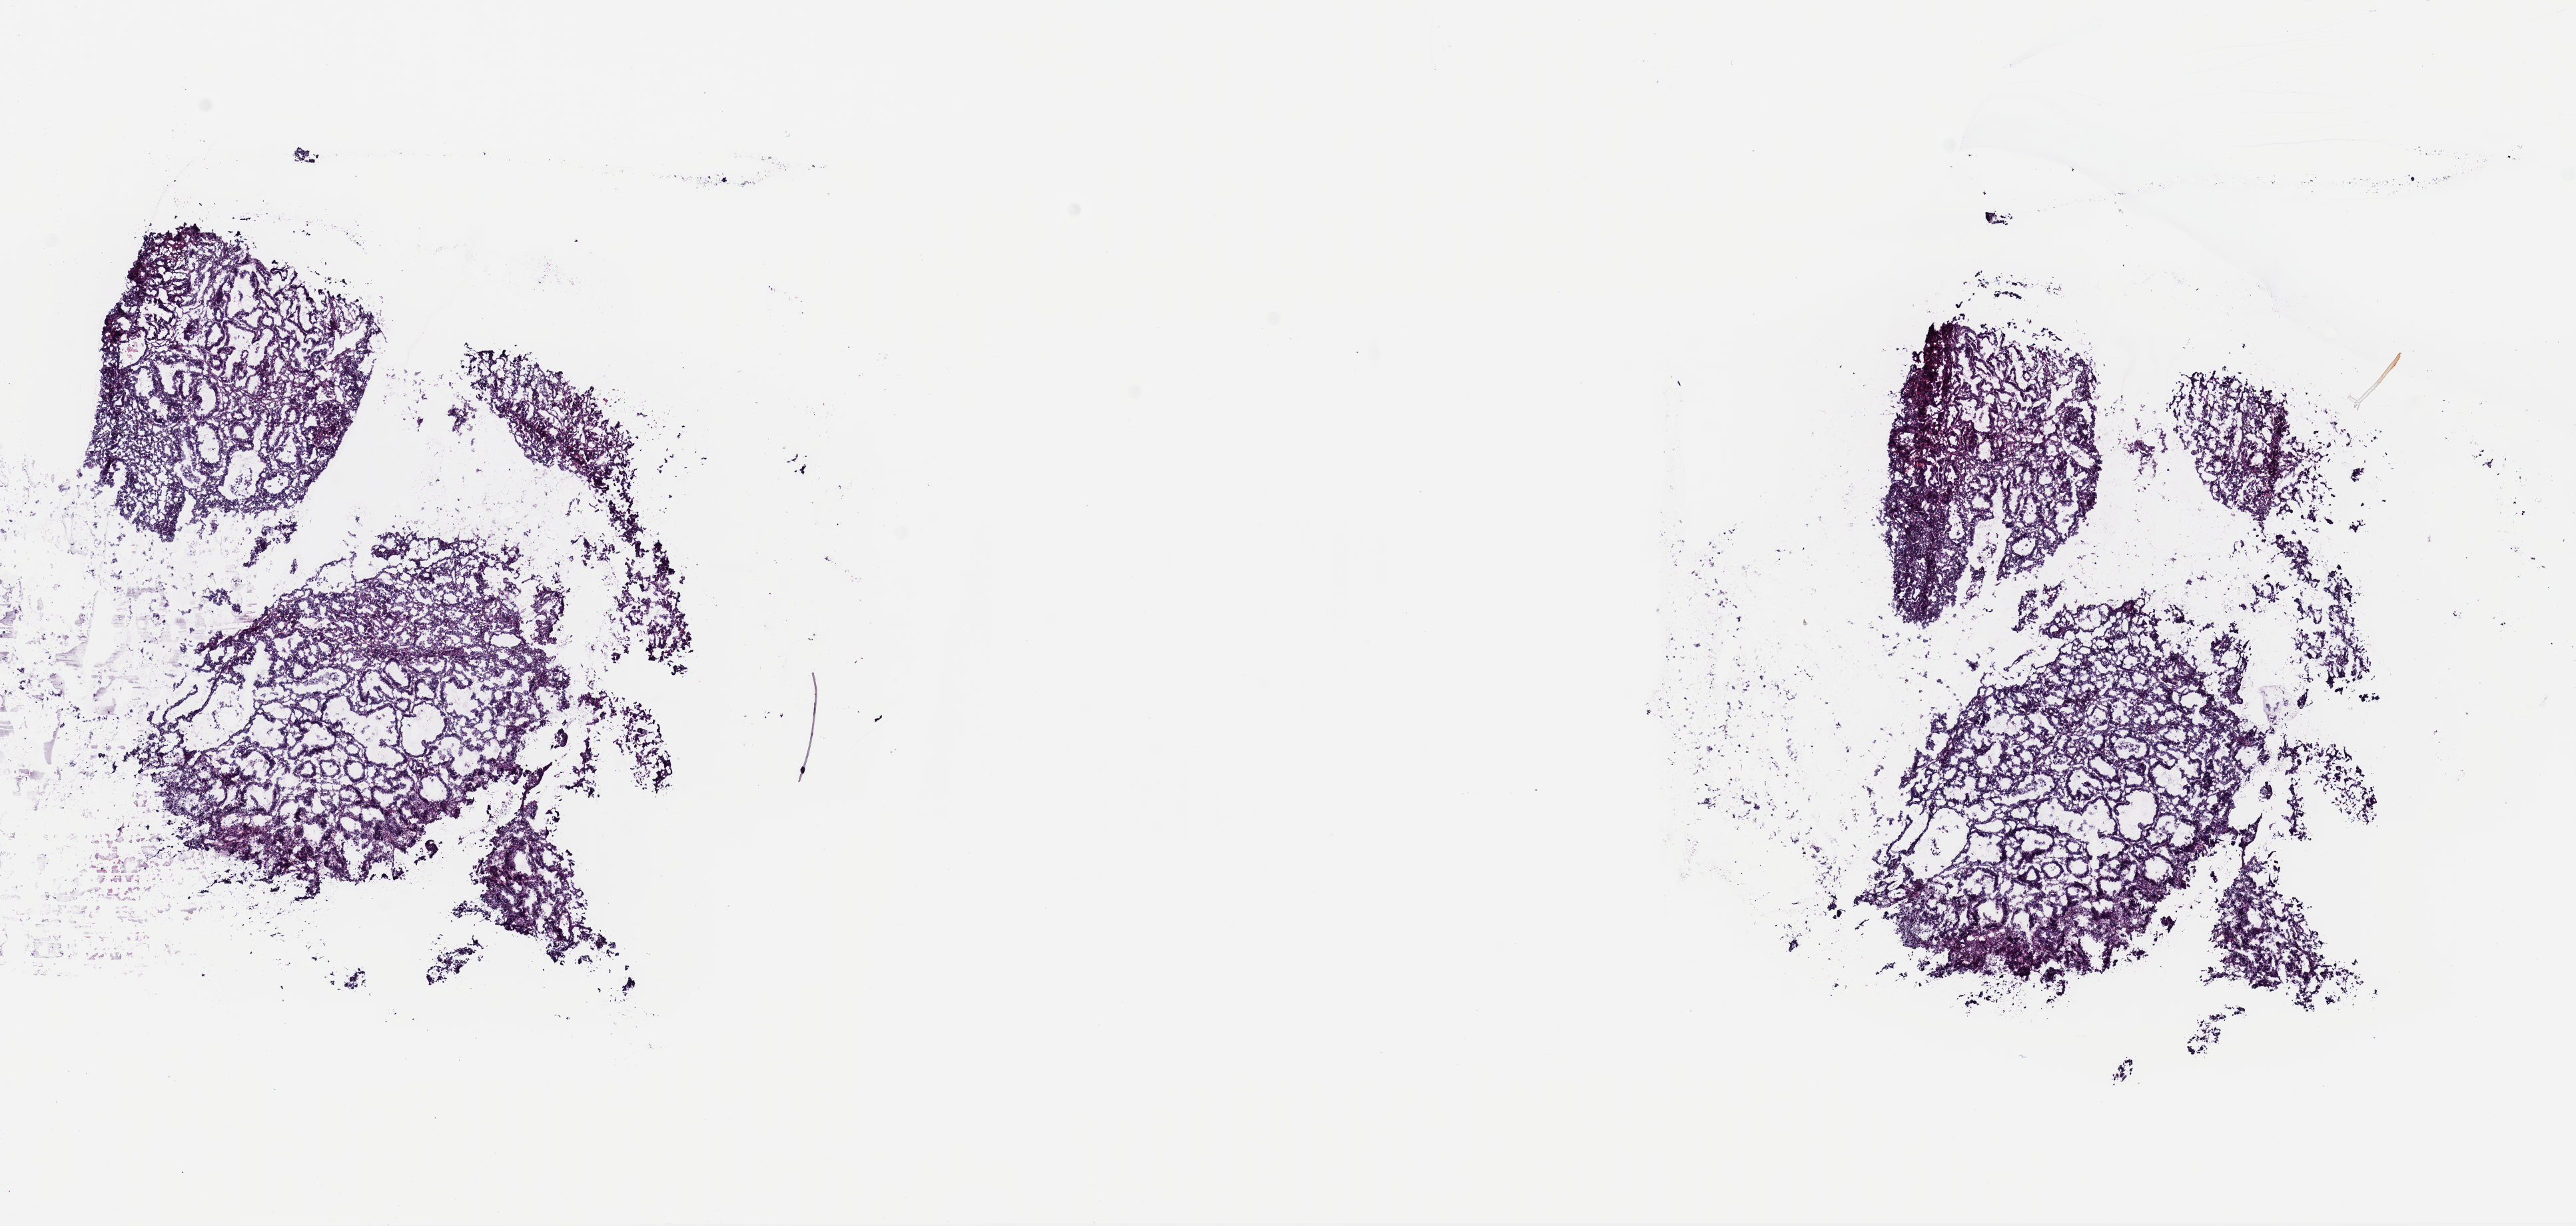
Whole-slide histology image, Hematoxylin and eosin (H&E) stained, shown as a low-resolution overview of the whole scanned area (about 15.3 x 7.3 mm, slide scanned at 40x); frozen section from the top of the tissue portion; primary tumour sample from the uterus. Patient: female, age at initial diagnosis 56 years. Histologic grade: G3 (poorly differentiated). Composition of this section per pathologist review: tumour cells 97%, tumour nuclei 95%, normal cells 0%, stromal cells 0%, necrosis 3%. Inflammatory infiltration, as recorded: lymphocyte infiltration 1%, monocyte infiltration 2%, neutrophil infiltration 0%.
FIGO stage: IB. Diagnosis: Endometrioid adenocarcinoma, NOS (endometrium).